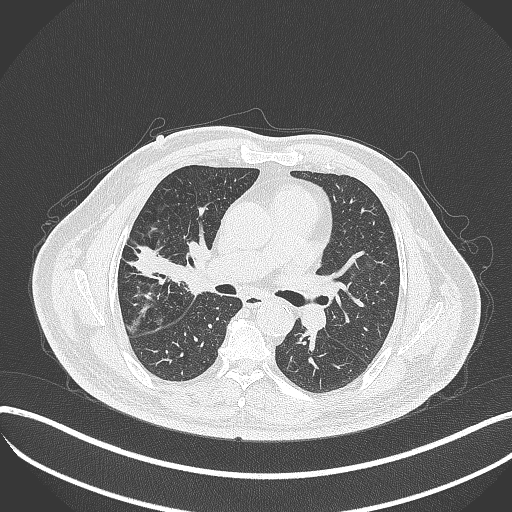
Chest CT, one axial slice; position 206 of 401 along the scan axis; reconstruction kernel B70f; lung window (W 1500 / L -600 HU); 1 mm slice thickness; 512 × 512 image matrix, field of view 400 × 400 mm. Patient: male, 72 years. Case-level facts recorded for this patient, not image findings: clinical TNM (as recorded): T1c N0 M0; histopathological grade: G2.
Outlined on this slice (rectangle marked by the reading radiologist):
- lung tumour (recorded histology: squamous cell carcinoma): box from (x=173, y=239) to (x=212, y=302) px